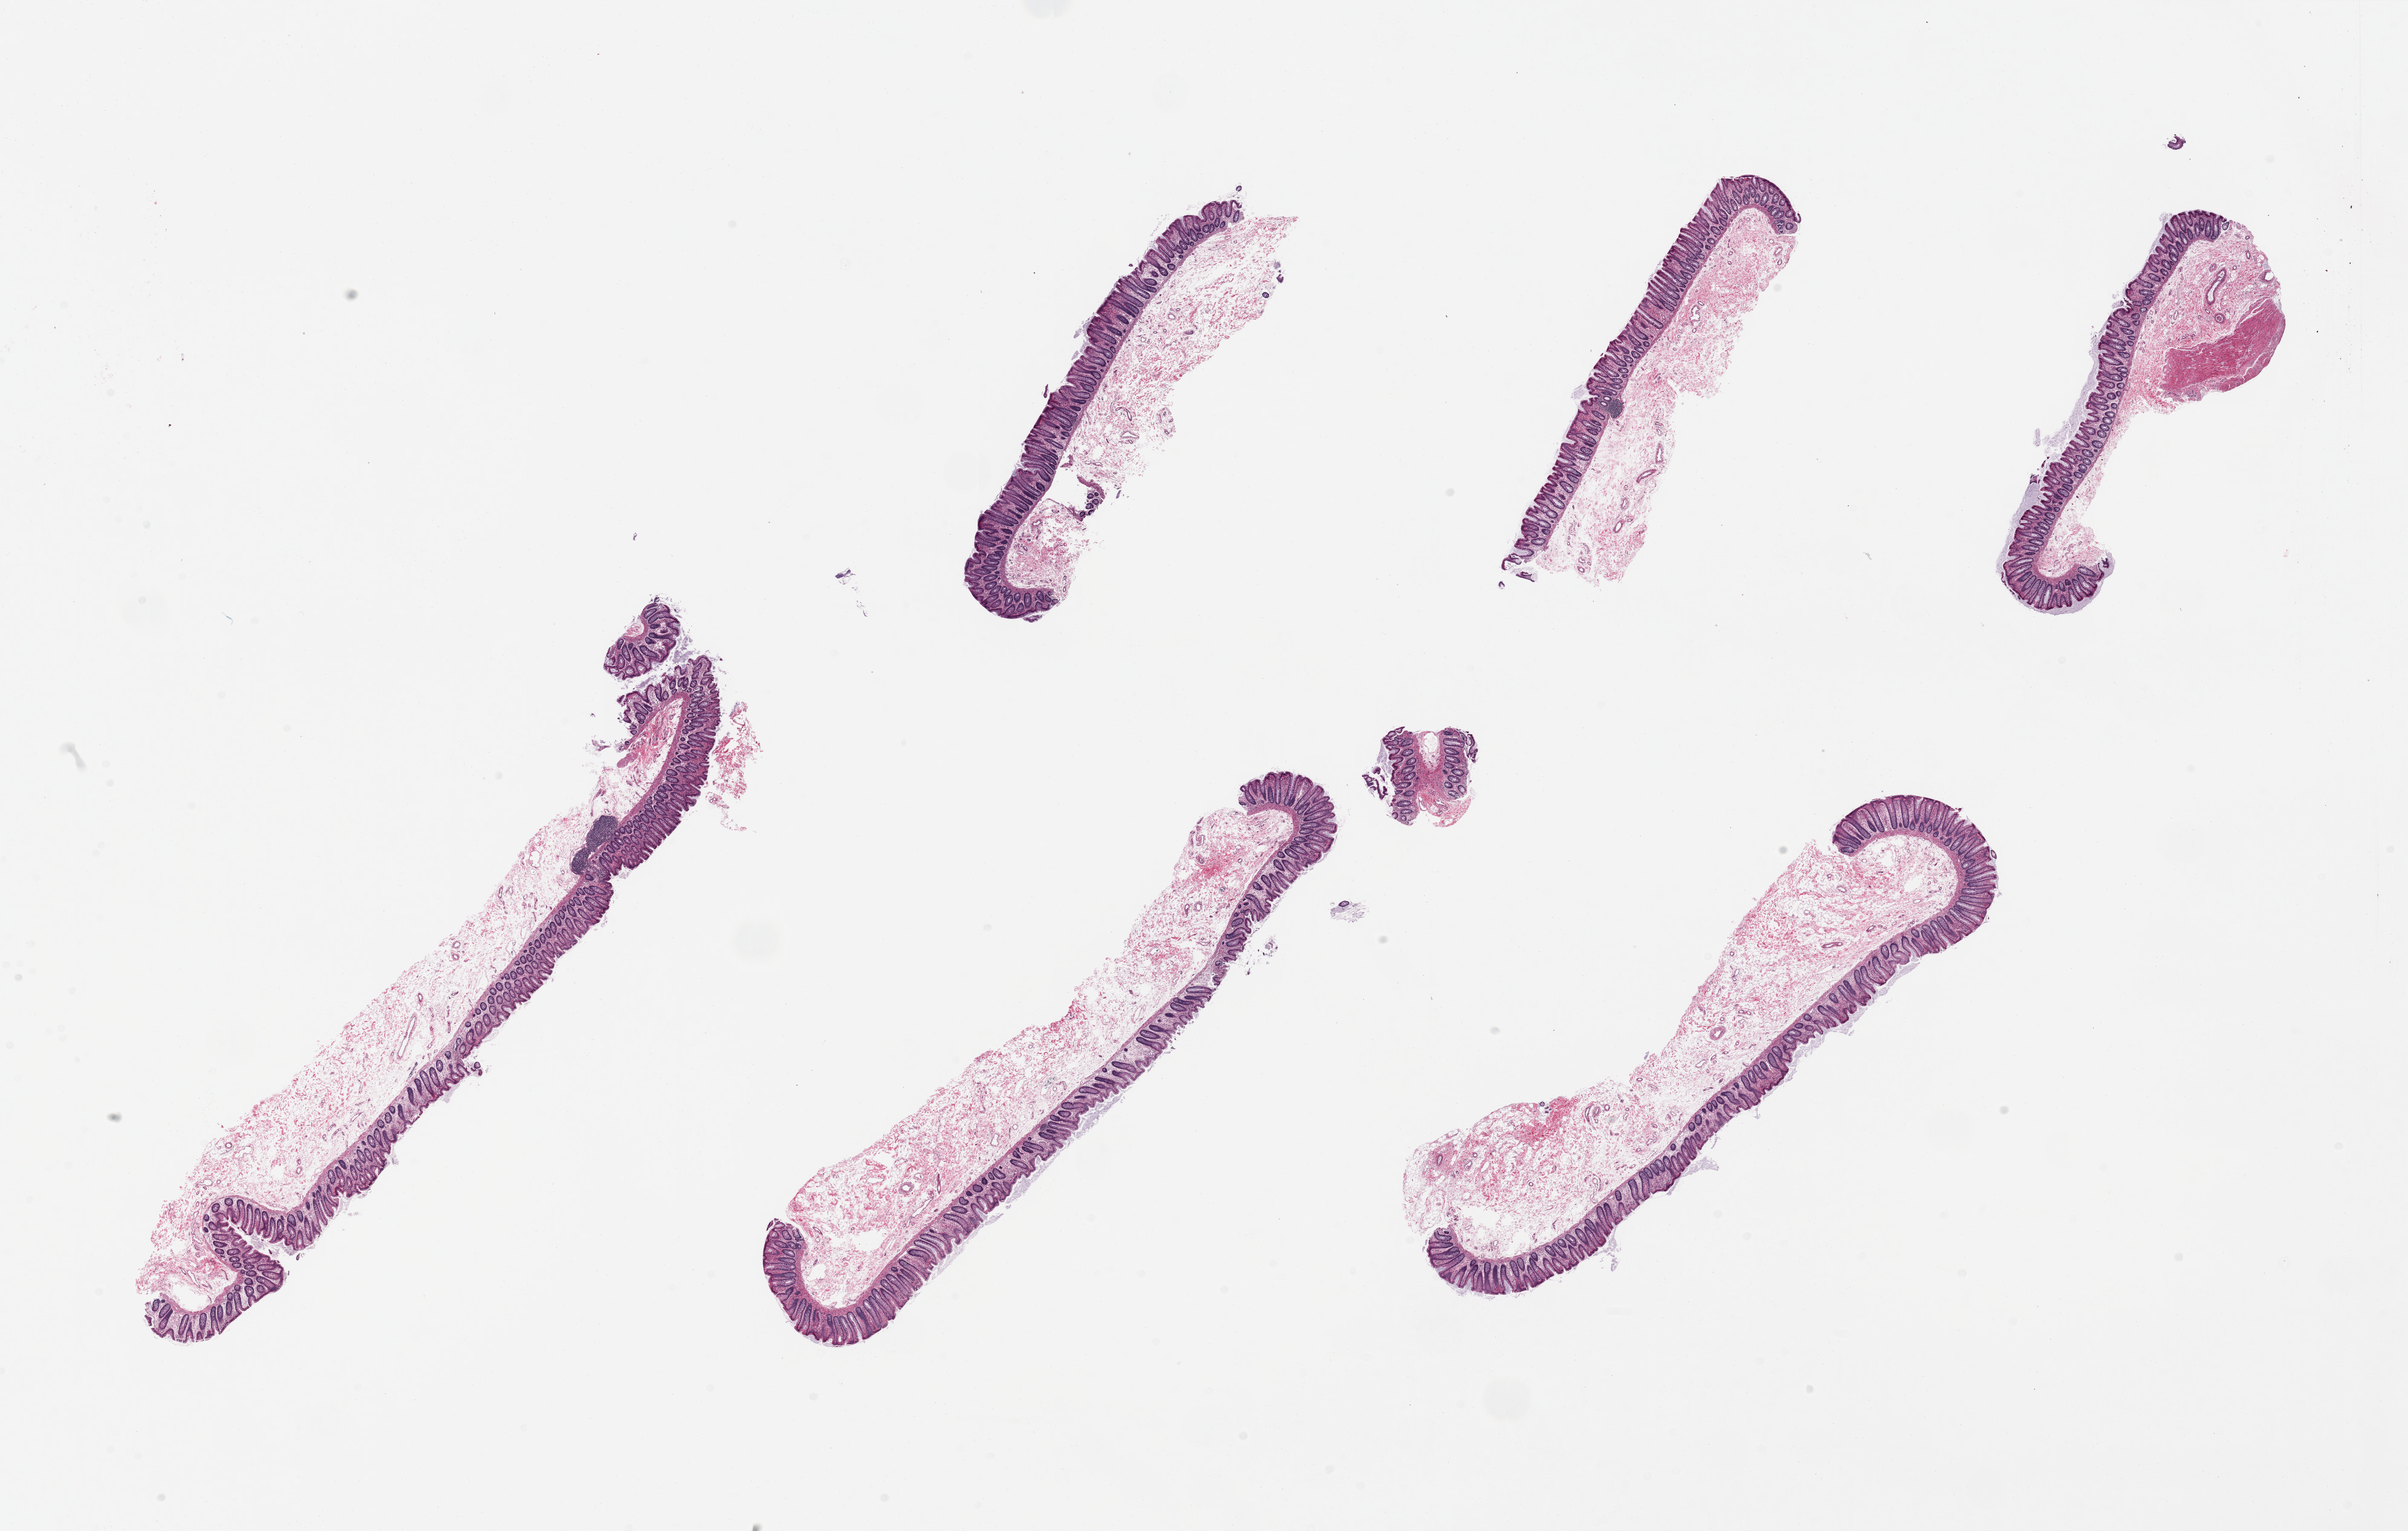
Digitized H&E-stained section — whole scanned area (about 31.5 x 20.0 mm) shown as a low-resolution overview; PAXgene-fixed, paraffin-embedded tissue; section of transverse colon (target tissue); tissue donor sample.
Pathologist's review note for this sample: 6 pieces. up to 12x3mm; Only 1 of 6 has muscularis. Transverse colon sample should have full thickness of wall.